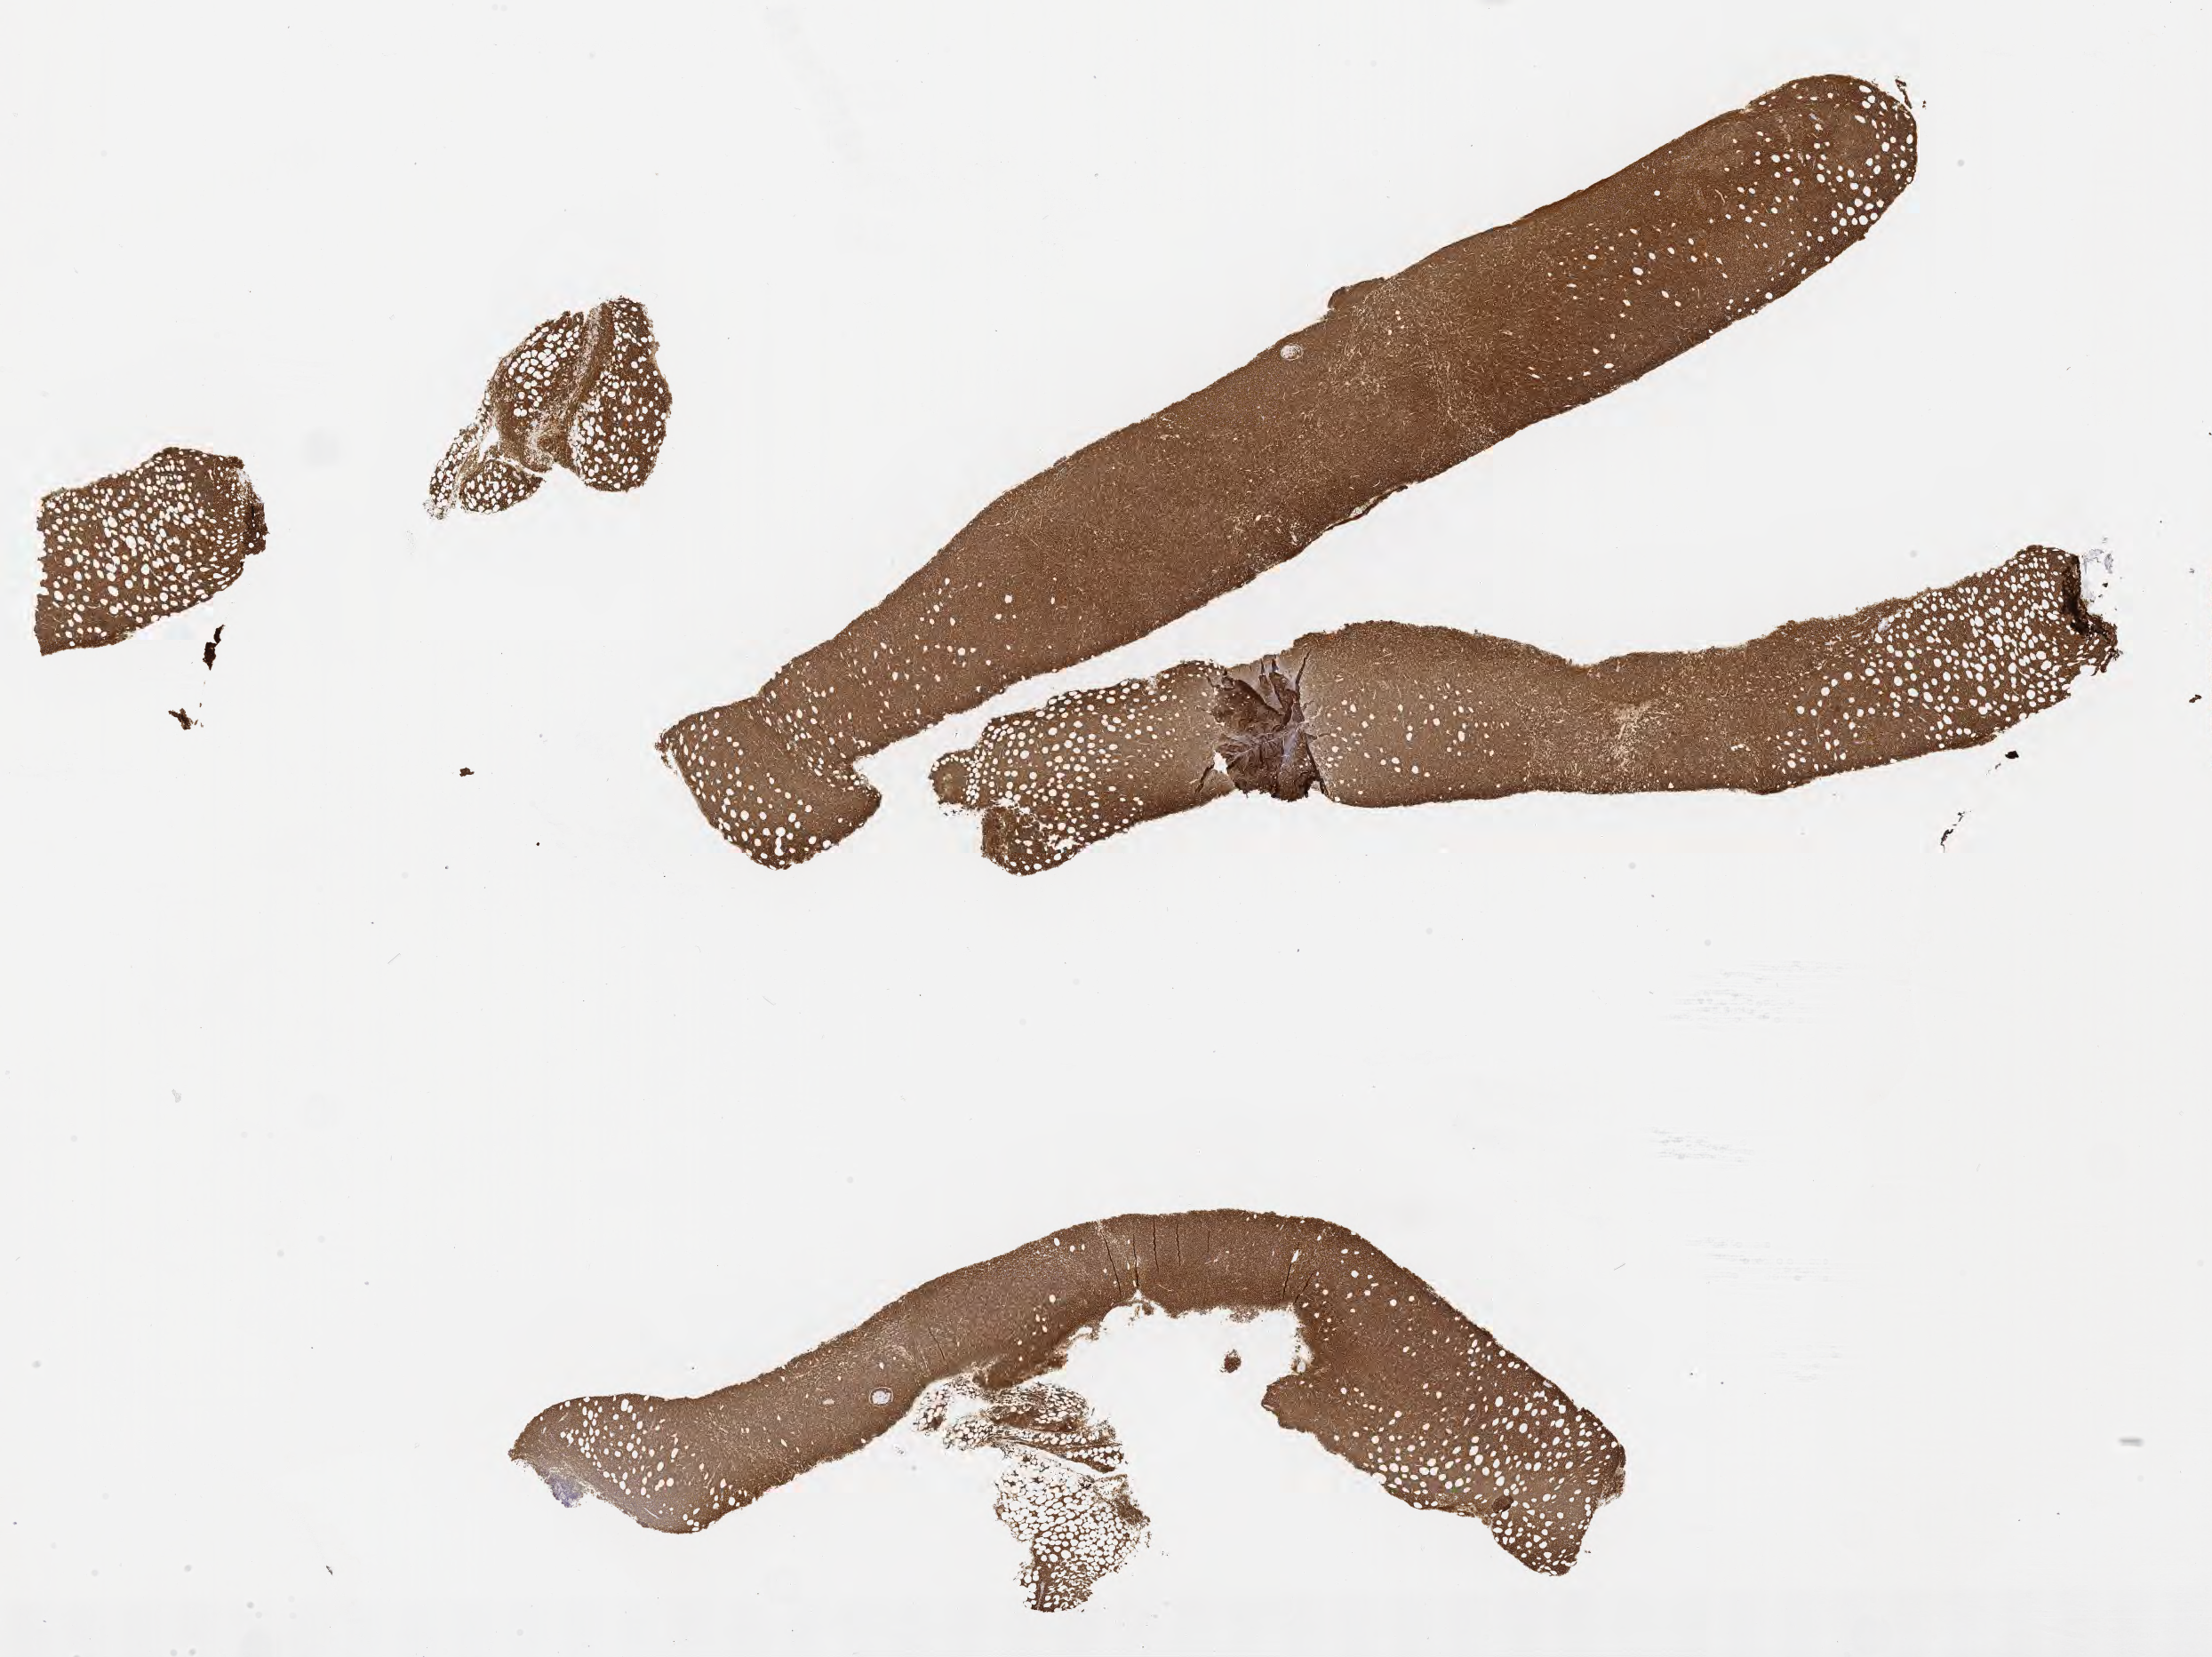
Whole-slide image, immunohistochemical stain for CD20 — whole scanned area (about 20.1 x 15.1 mm) shown as a low-resolution overview. Tumor tissue. Patient female; 43 years old.
Diagnosis: Burkitt lymphoma, NOS.